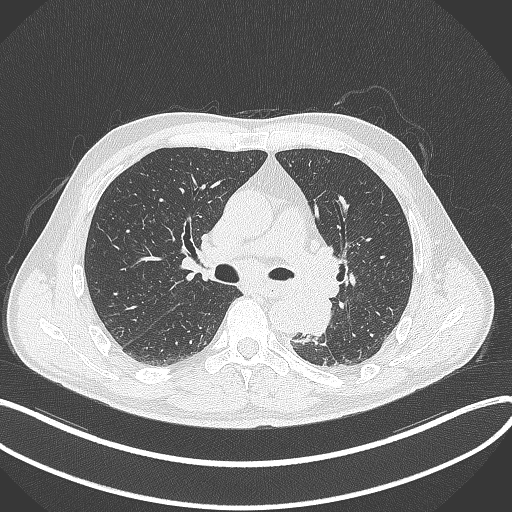
Chest CT, one axial slice; position 207 of 329 along the scan axis; lung window (W 1500 / L -600 HU); 512 × 512 image matrix, field of view 400 × 400 mm. Male patient, age 59 years. Case-level facts recorded for this patient, not image findings: clinical TNM (as recorded): T2a N2 M0.
Outlined on this slice (bounding box drawn by a radiologist):
- lung tumour (recorded histology: squamous cell carcinoma): box from (x=299, y=291) to (x=335, y=339) px